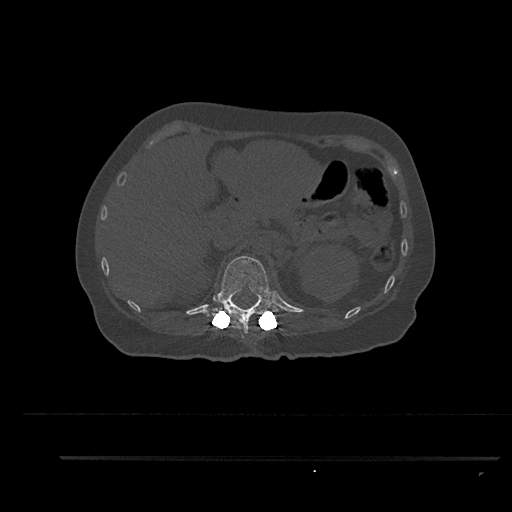
CT including the spine, one axial slice. Slice 260 of 797 in the series (ordered by position). Reconstruction kernel Br40s/3. 120 kVp. Bone window (W 1800 / L 400 HU). 0.5 mm slice thickness. 512 × 512 image matrix, field of view 408 × 408 mm. Female patient, age 44 years. From the clinical record (not read from this slice): primary cancer: renal.
Structures marked on this image (semi-automatically segmented with operator editing):
- T12 vertebra: bounding box [x1, y1, x2, y2] px = [204, 256, 282, 339]